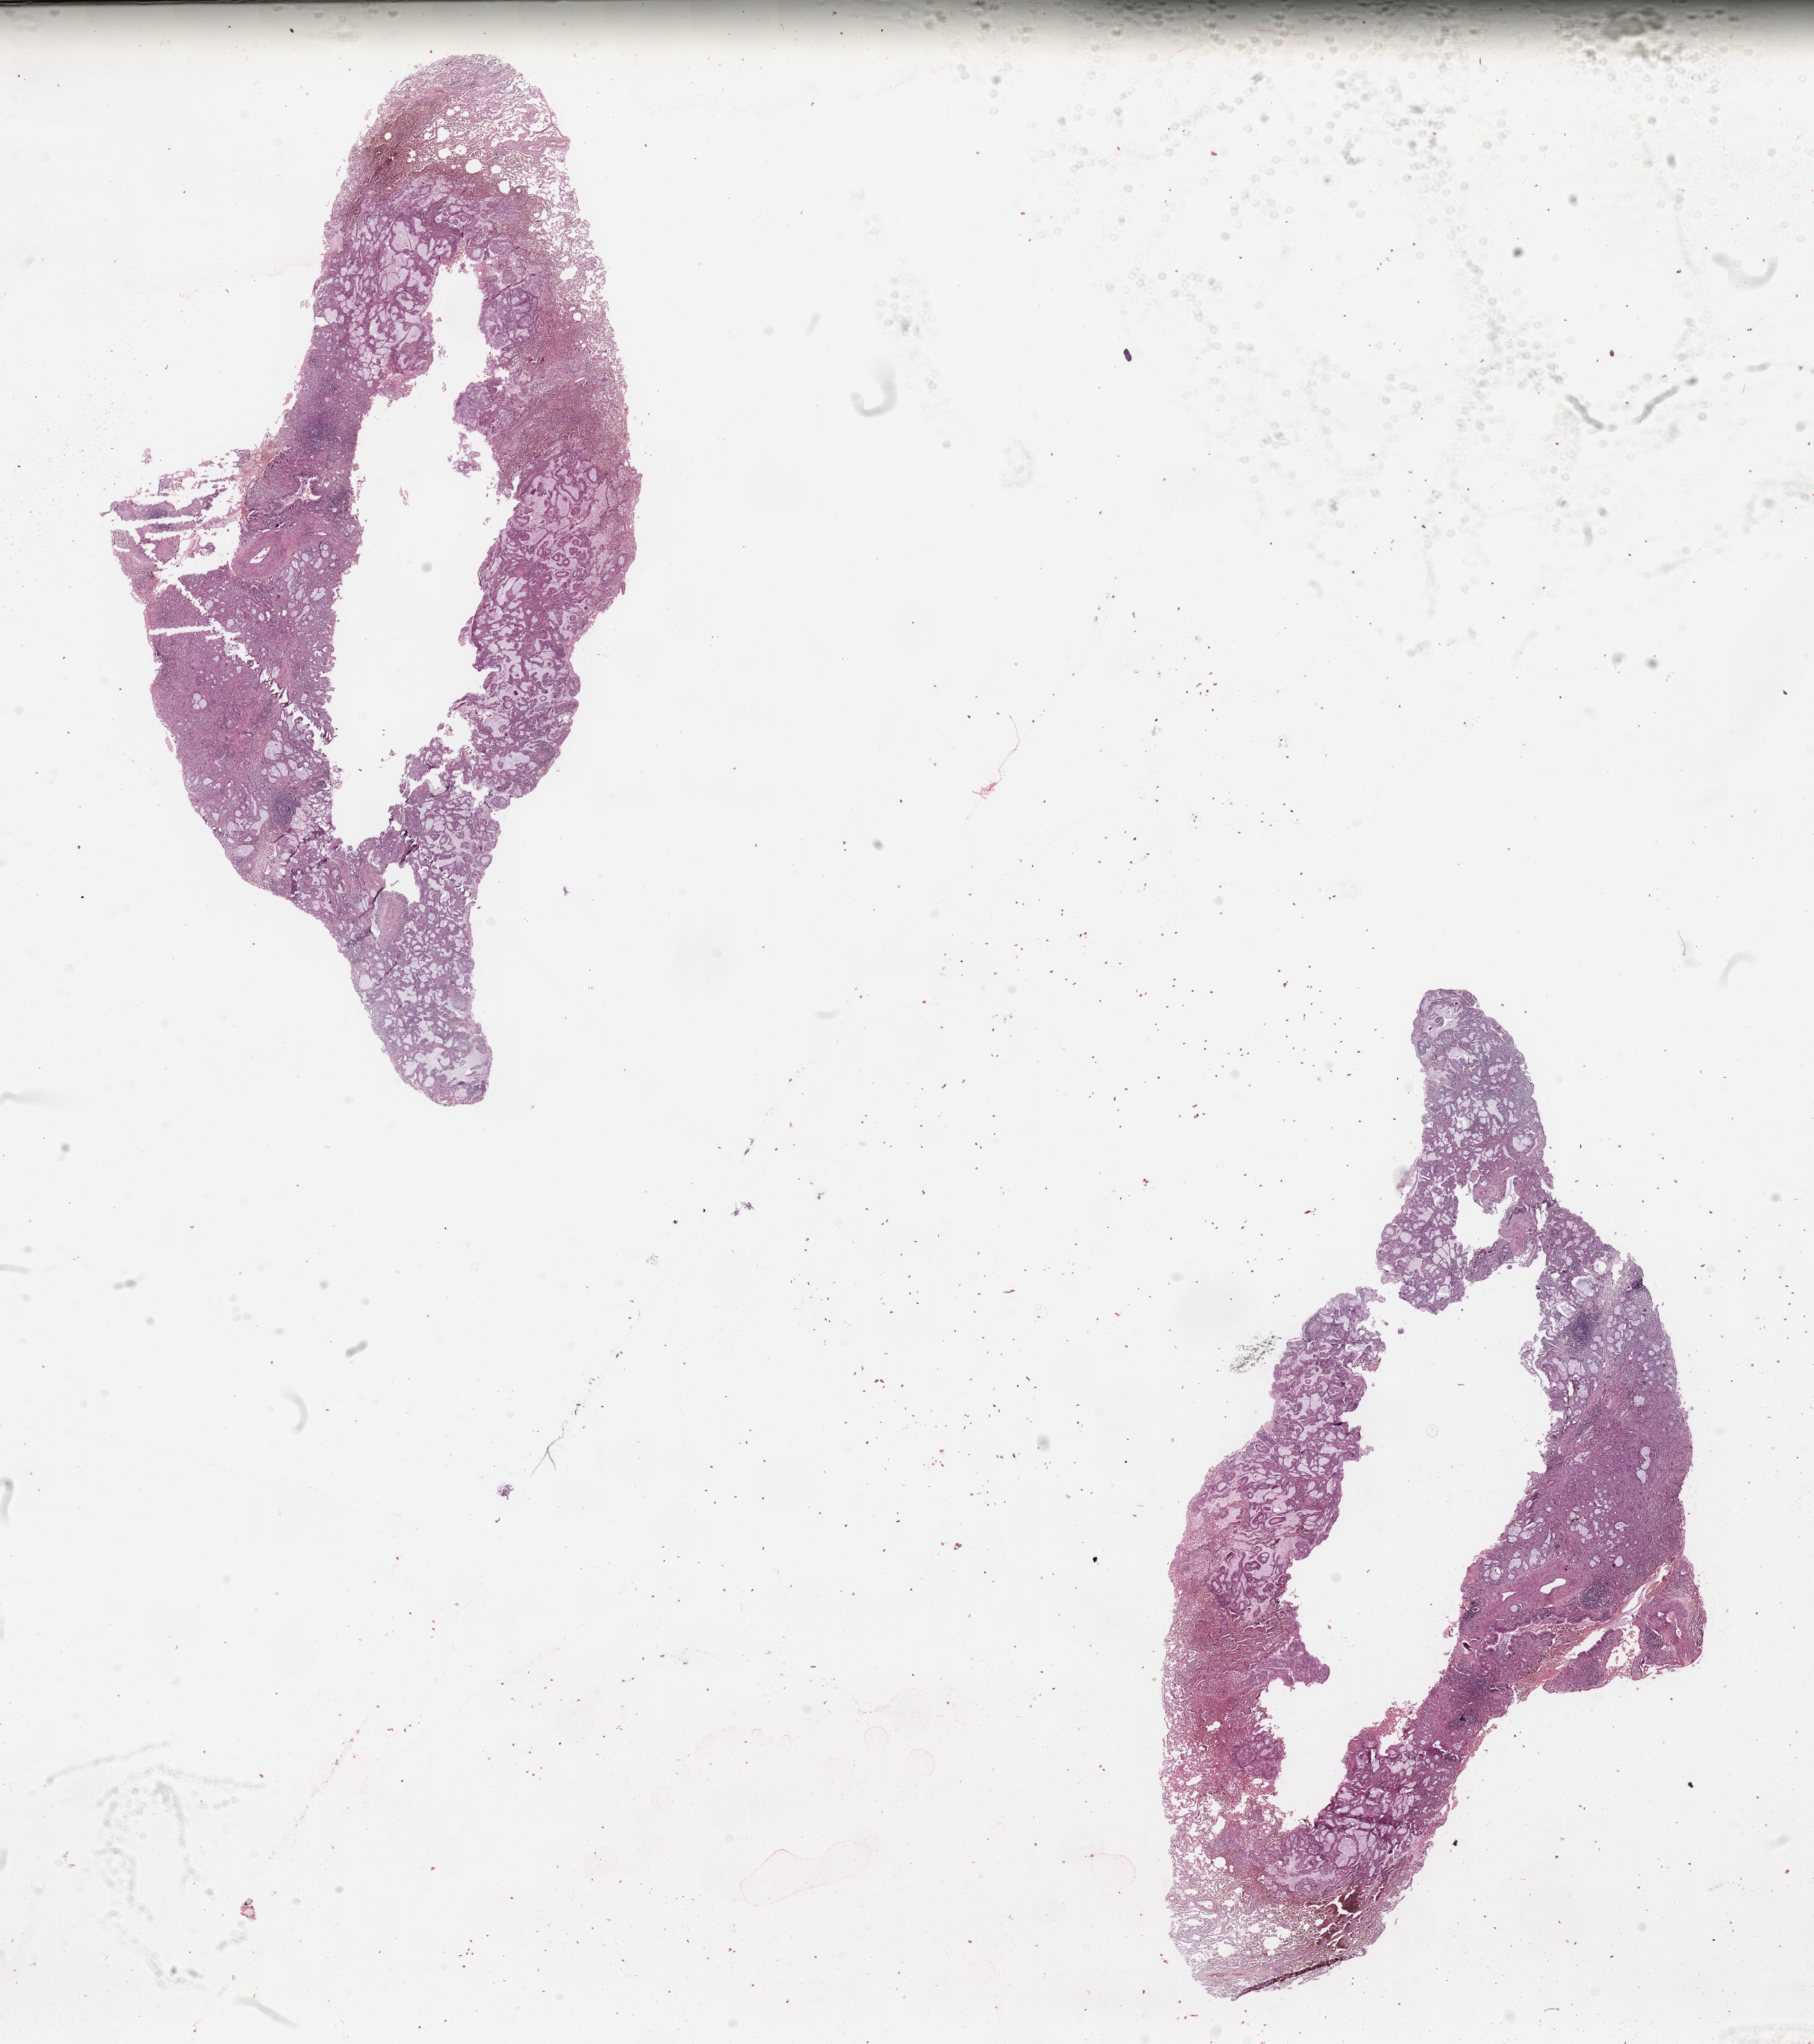
Hematoxylin and eosin (H&E) stained whole-slide image — a low-resolution overview of the entire scanned area, about 20.7 x 23.3 mm, lung, tumour tissue. 47-year-old male patient. Histologic grade: G2 (moderately differentiated).
Diagnosis: Adenocarcinoma, NOS. Primary tumour site (as recorded): right upper lobe. AJCC pathologic stage: IIA.